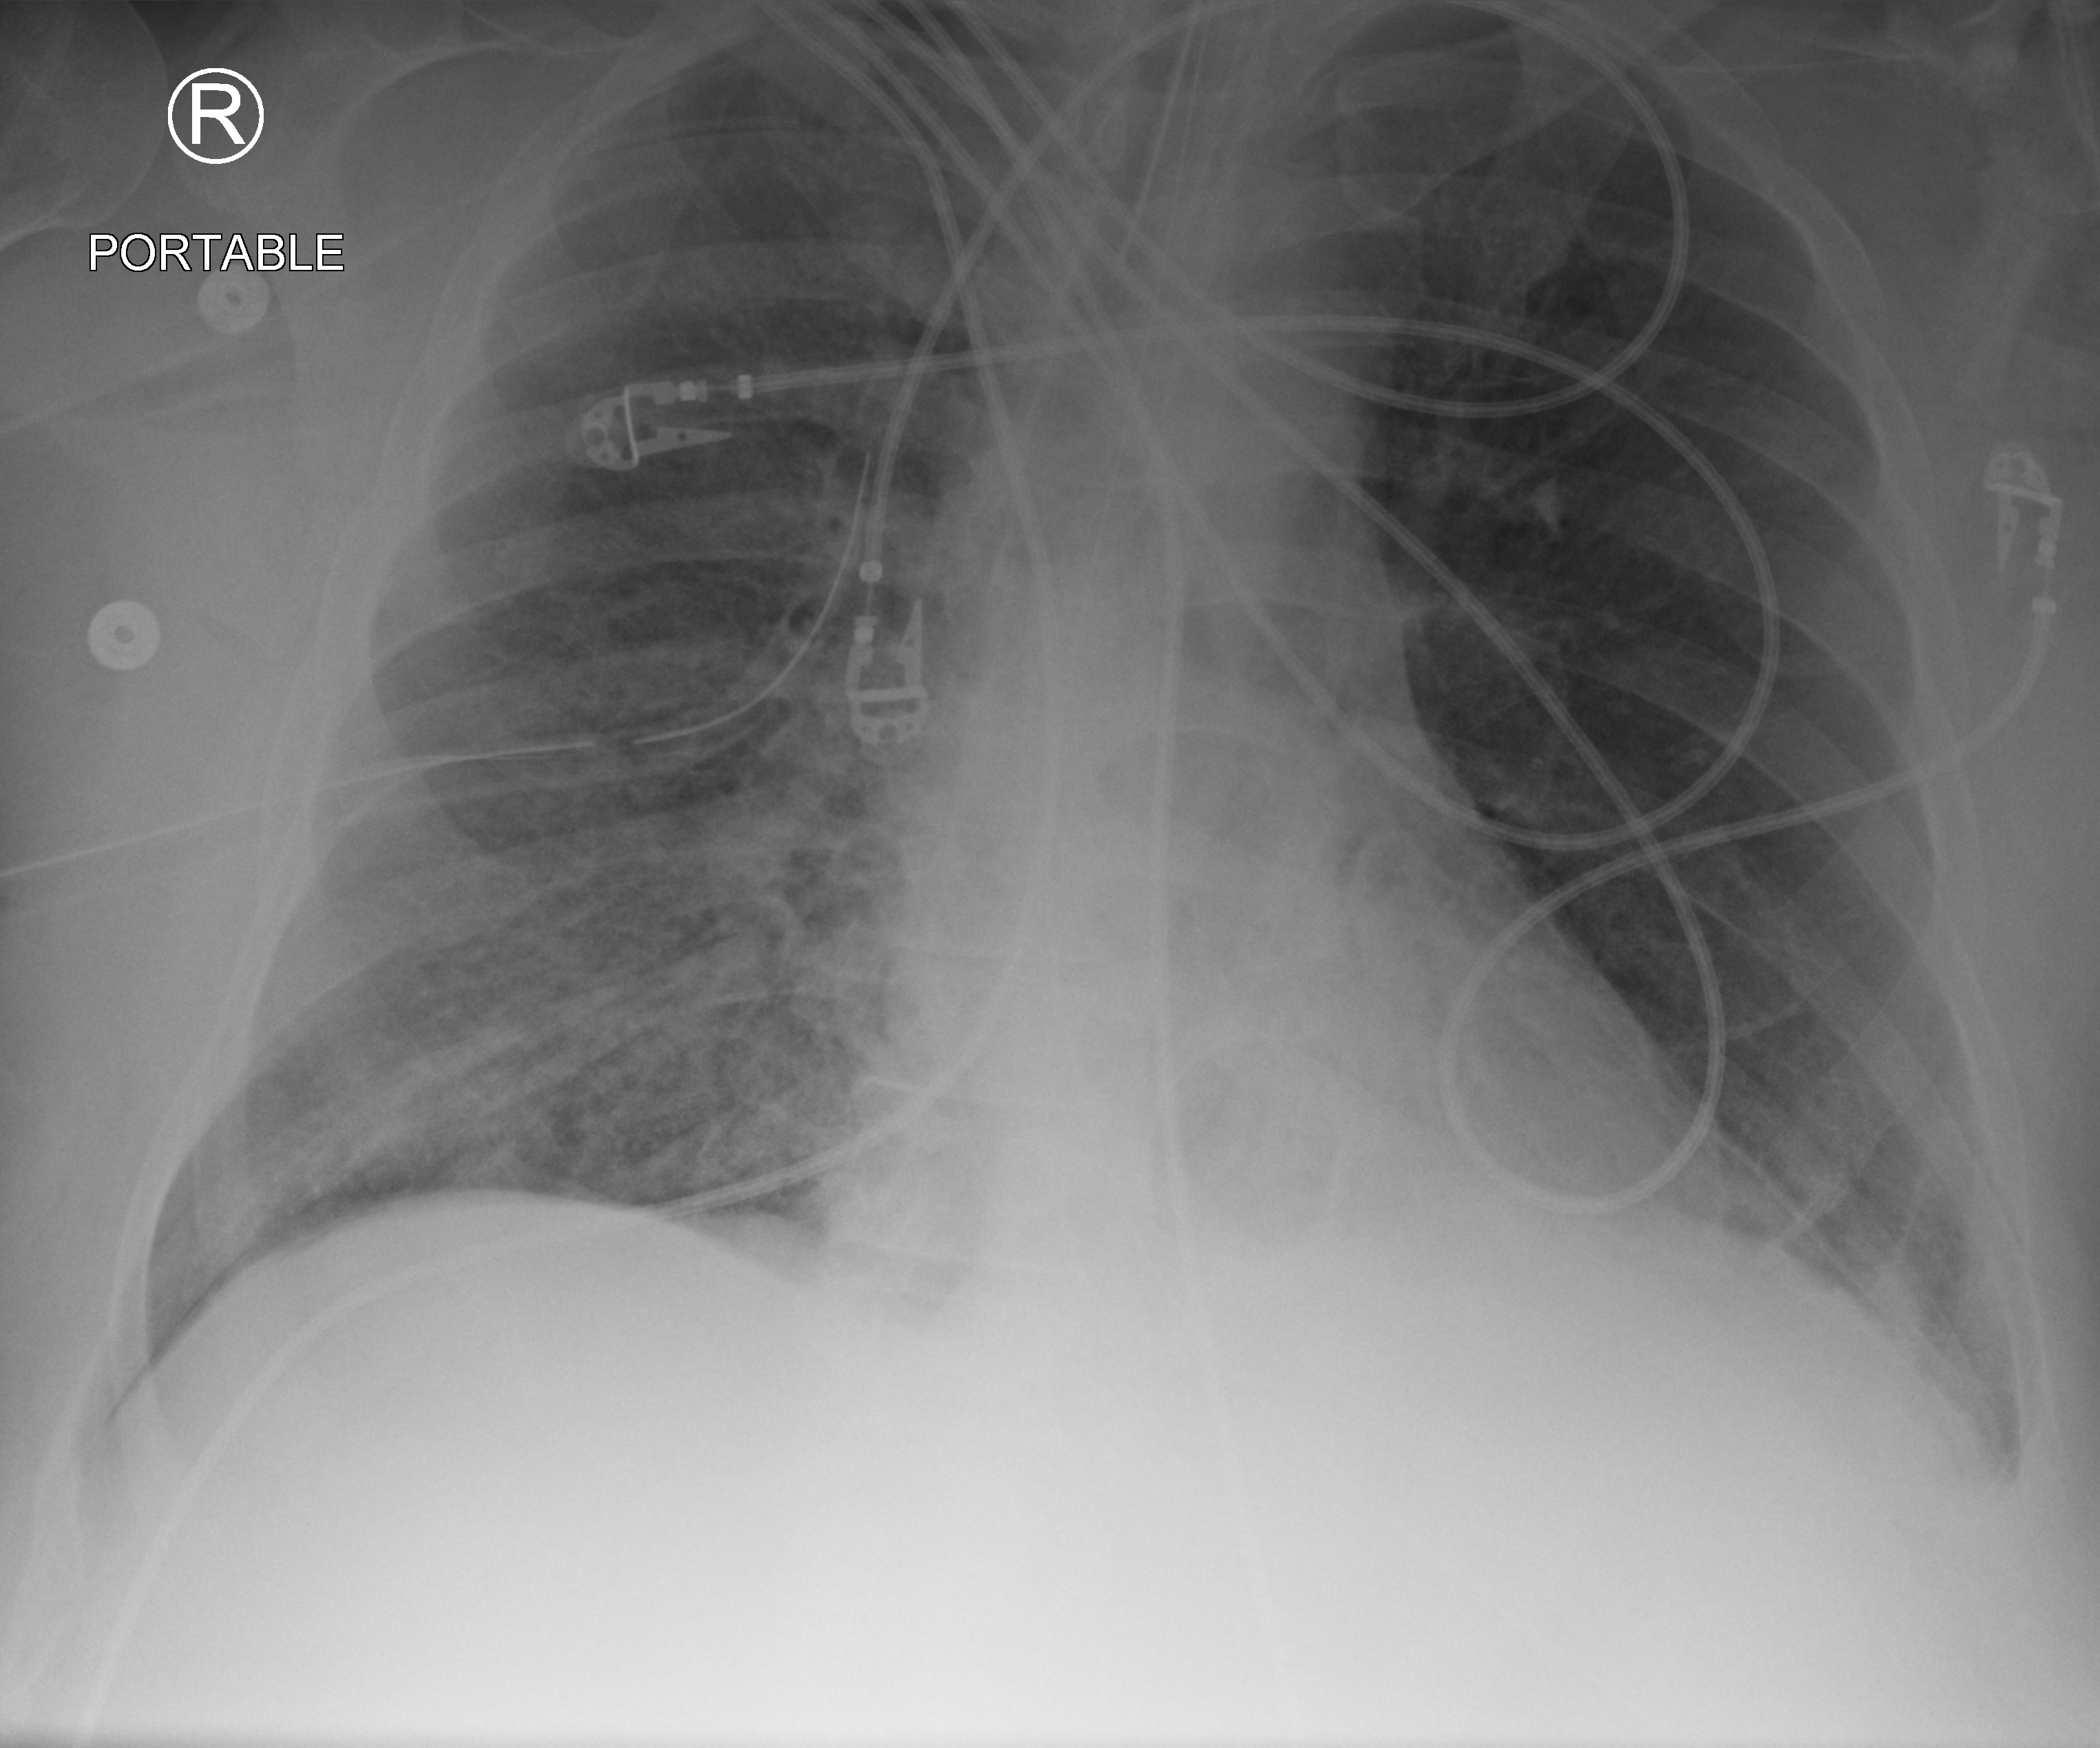
Bedside chest radiograph (computed radiography); anteroposterior (AP) projection. Patient hospitalised with COVID-19, aged 18–59 years.
Hospital-stay facts (about this admission, not read from this image; timing relative to this image not recorded): length of hospital stay: 26 days; chronic kidney disease (admission record): no.